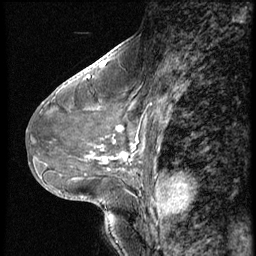
Breast MRI (dynamic contrast-enhanced), one sagittal slice; slice 28 of 56 in the series (ordered by position); dynamic contrast-enhanced series, image 2 of 3 at this slice position (ordered by acquisition); 1.5 T; TE 4.2 ms, TR 9 ms; 2.5 mm slice thickness; 256 × 256 image matrix, field of view 180 × 180 mm. Female patient, age 46 years. From the clinical record (not read from this slice): setting: breast cancer imaged before/during neoadjuvant chemotherapy; receptor status: HER2-positive.
Structures marked on this image (semi-automatically segmented with operator editing):
- analysis volume of interest (the breast-tissue region the enhancement analysis was run in; not a lesion): box from (x=64, y=98) to (x=174, y=182) px
- tumour enhancement mask (voxels above the 140 % enhancement threshold inside the analysis volume of interest): (x=124, y=156)–(x=174, y=179)